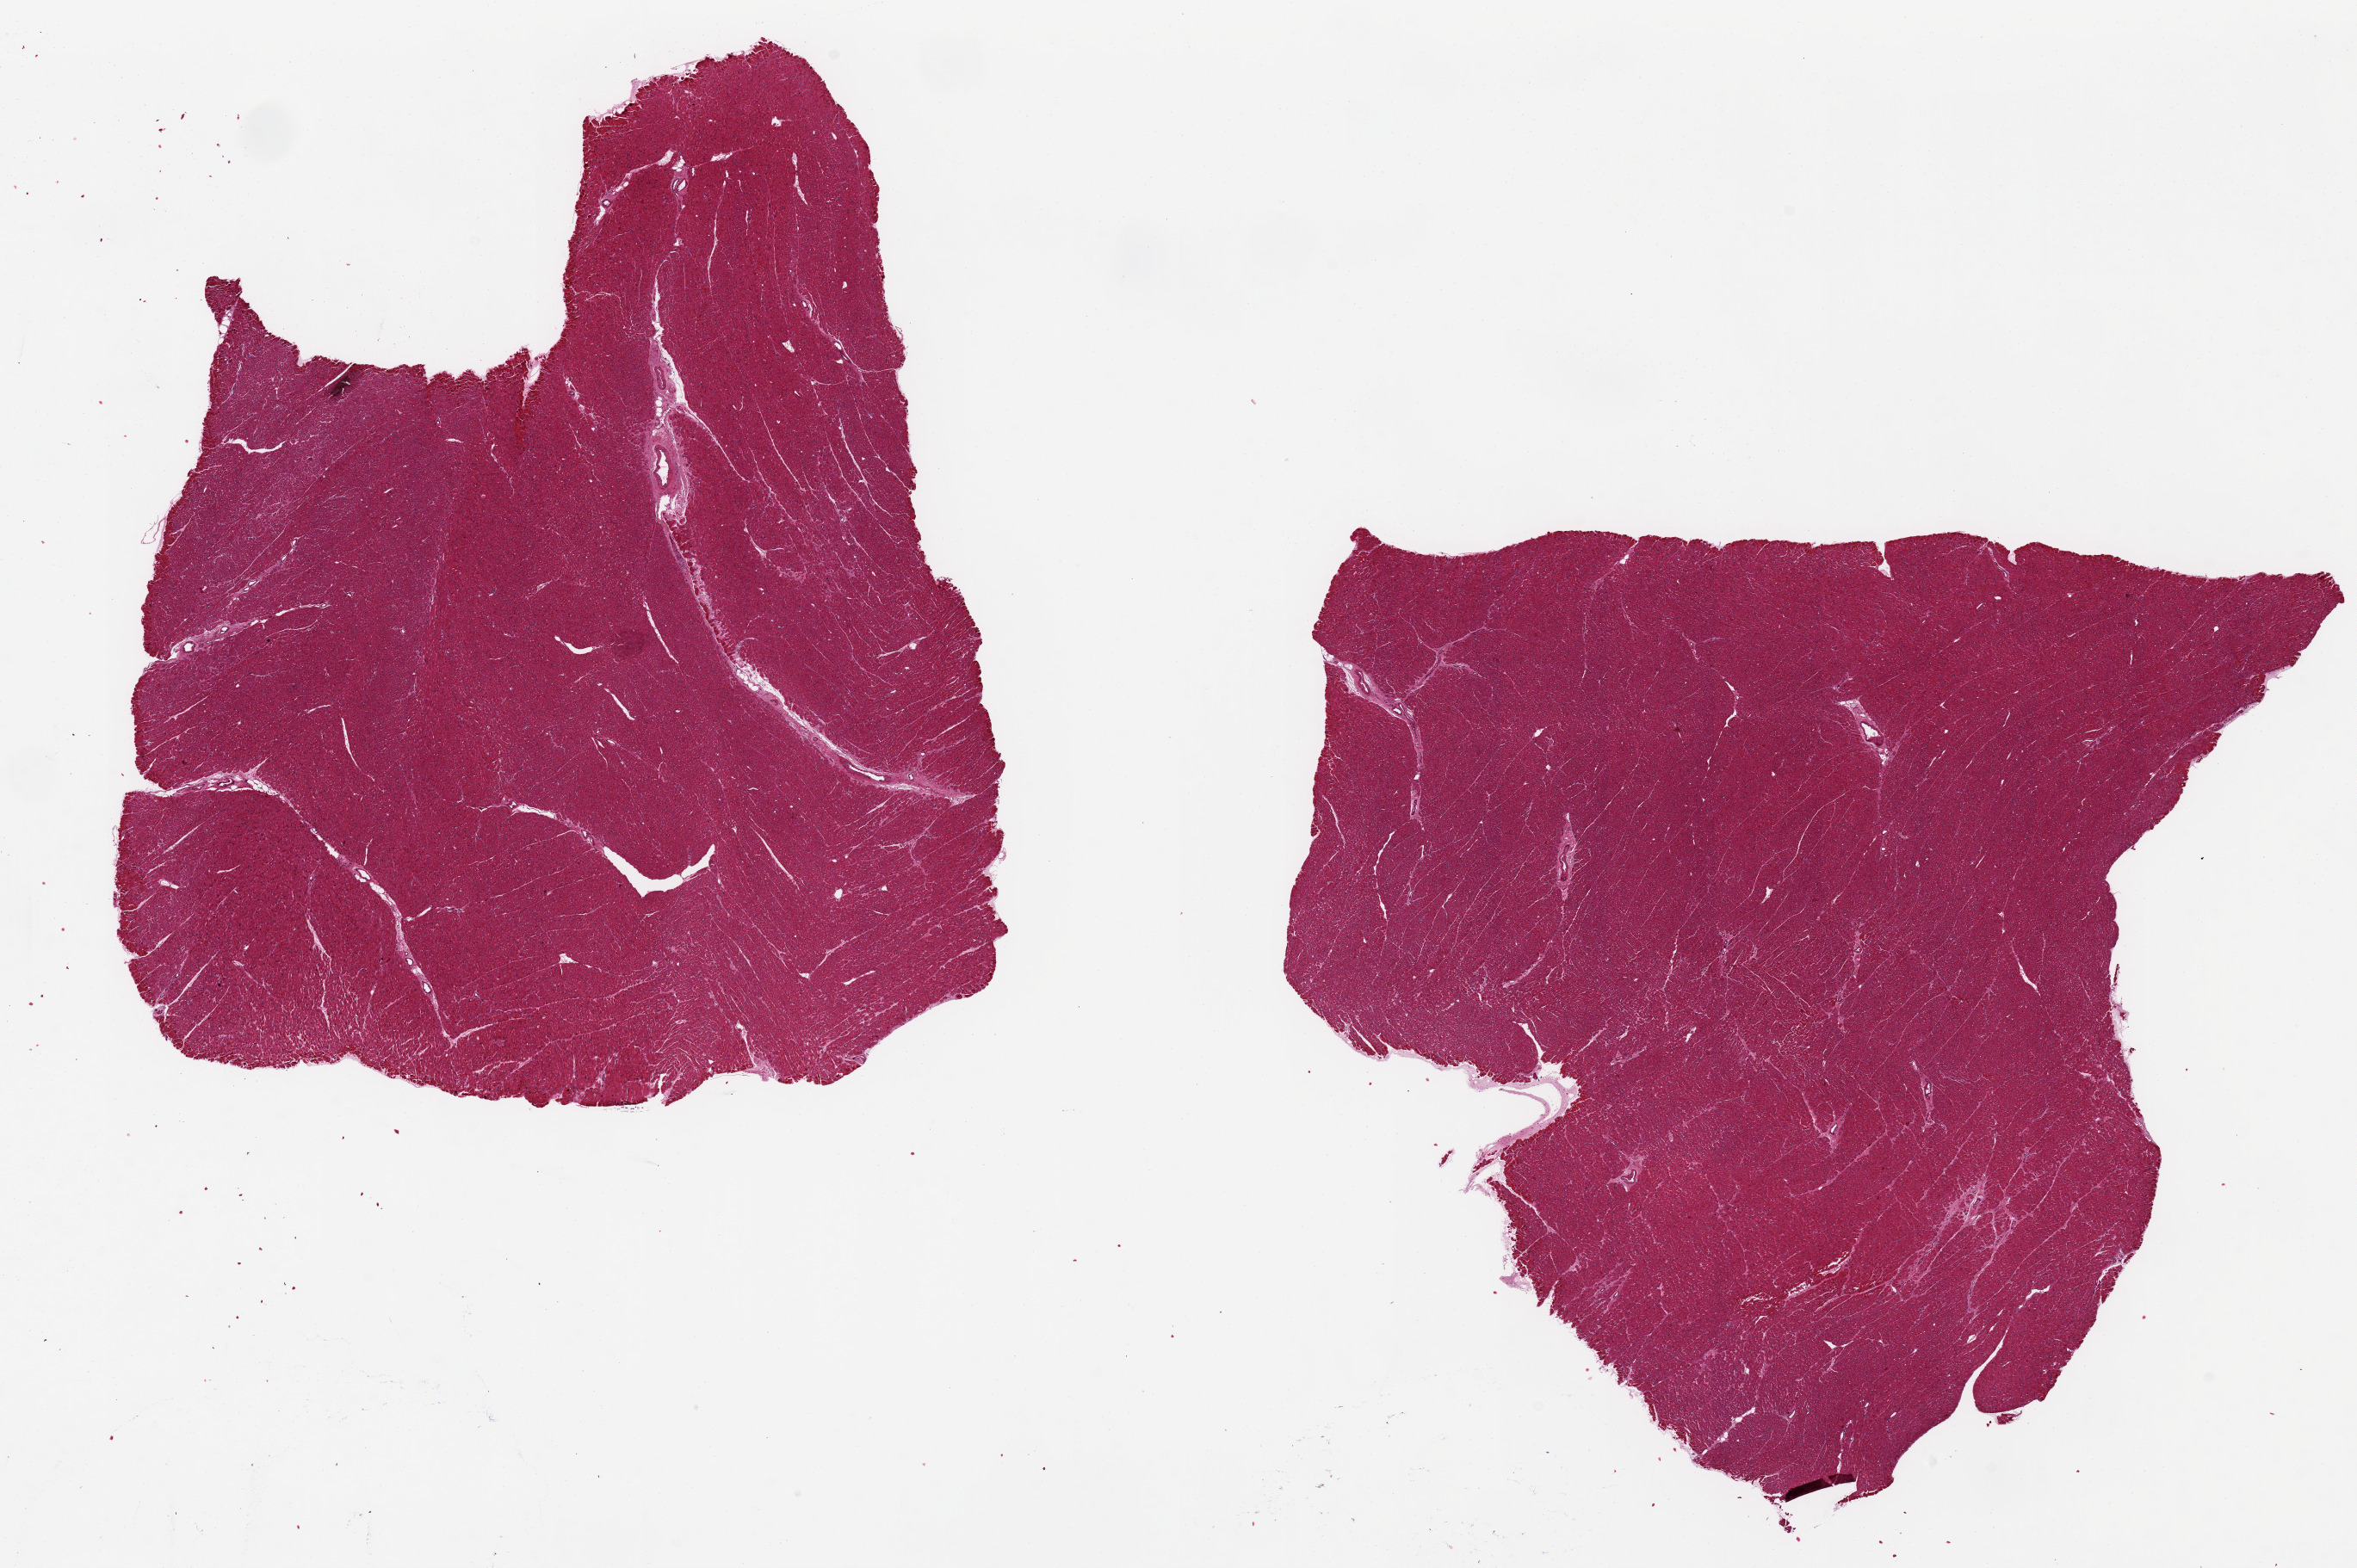
H&E whole-slide image, brightfield, whole scanned area (about 21.7 x 14.4 mm) shown as a low-resolution overview; PAXgene-fixed, paraffin-embedded tissue; target tissue: heart; tissue donor sample. Donor sex: male.
Pathologist's review note for this sample: 2 ~9x8mm aliquots, minimal ischemic changes.